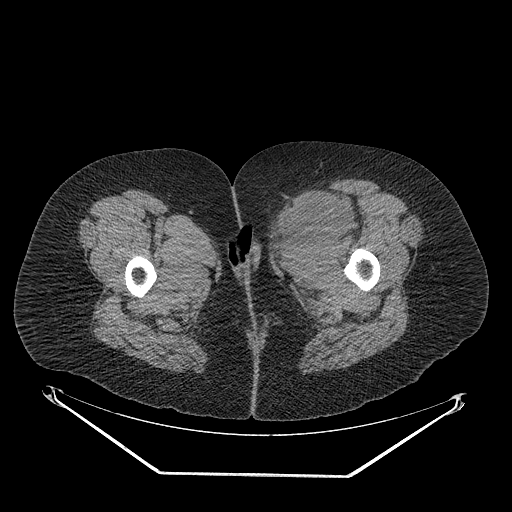
CT of an extremity soft-tissue mass (from a PET/CT study), one axial slice. Slice 38 of 267 in the series (ordered by position). 140 kVp. Soft-tissue window (W 400 / L 40 HU). 512 × 512 image matrix, field of view 500 × 500 mm. Female patient. From the clinical record (not read from this slice): histological type: myxofibrosarcoma; grade: intermediate; site of the primary tumour: left thigh.
Structures marked on this image (expert contour drawn on MRI and transferred to this co-registered scan by the dataset authors):
- gross tumour volume including surrounding oedema: bounding box (x1, y1, x2, y2) in pixels: (267, 192, 359, 257)
- gross tumour volume (mass): (274, 192, 348, 243)